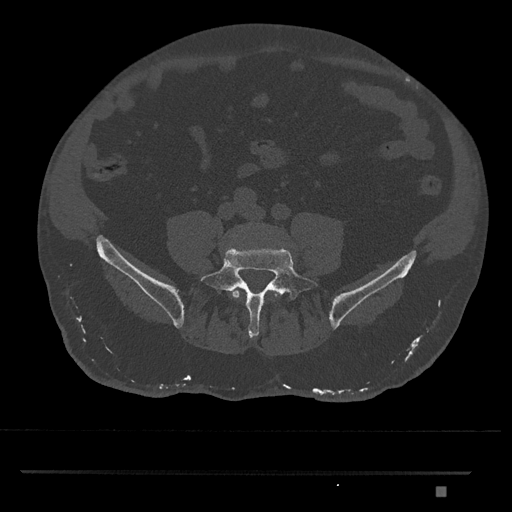
CT including the spine, one axial slice. Slice 567 of 1134 in the series (ordered by position). Reconstruction kernel Br40s/3. 120 kVp. Bone window (W 1800 / L 400 HU). 0.5 mm slice thickness. 512 × 512 image matrix, field of view 429 × 429 mm. Male patient, age 65 years. From the clinical record (not read from this slice): primary cancer: prostate.
Structures marked on this image (semi-automatic segmentation, software-assisted and operator-edited):
- L4 vertebra: bounding box [x1, y1, x2, y2] px = [229, 288, 281, 300]
- L5 vertebra: [200, 247, 320, 339]